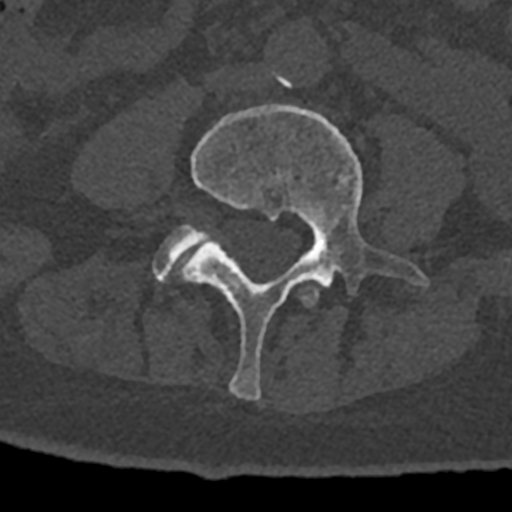
CT including the spine, one axial slice; slice 254 of 797 in the series (ordered by position); reconstruction kernel Br40s/3; 120 kVp; bone window (W 1800 / L 400 HU); 0.5 mm slice thickness; 512 × 512 image matrix, field of view 160 × 160 mm. Patient: male, 74 years. From the clinical record (not read from this slice): primary cancer: renal; vertebrae with lytic lesions (as recorded): T10, L1, L2, L3, L4, L5.
Structures marked on this image (semi-automatically segmented with operator editing):
- L3 vertebra: bounding box (x1, y1, x2, y2) in pixels: (300, 287, 319, 306)
- L4 vertebra: (179, 105, 429, 400)
- L5 vertebra: (153, 225, 208, 281)